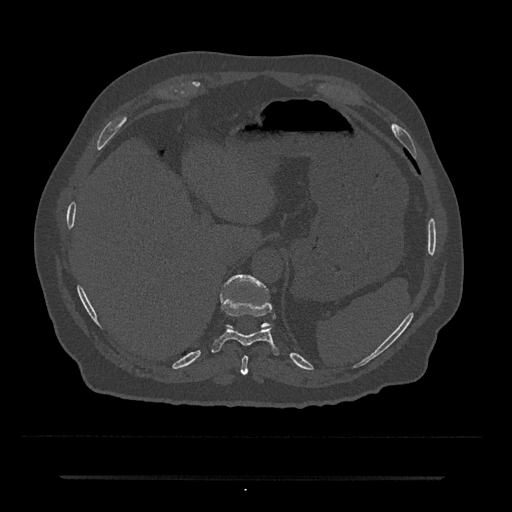
CT including the spine, one axial slice; slice 225 of 797 in the series (ordered by position); reconstruction kernel Br40s/3; 120 kVp; bone window (W 1800 / L 400 HU); 512 × 512 image matrix, field of view 437 × 437 mm. Male patient, age 69 years. From the clinical record (not read from this slice): primary cancer: prostate.
Annotated regions visible in this slice (semi-automatic segmentation, software-assisted and operator-edited):
- T10 vertebra: bounding box [x1, y1, x2, y2] px = [211, 277, 279, 355]
- T11 vertebra: [224, 274, 270, 328]
- T9 vertebra: [241, 355, 248, 375]